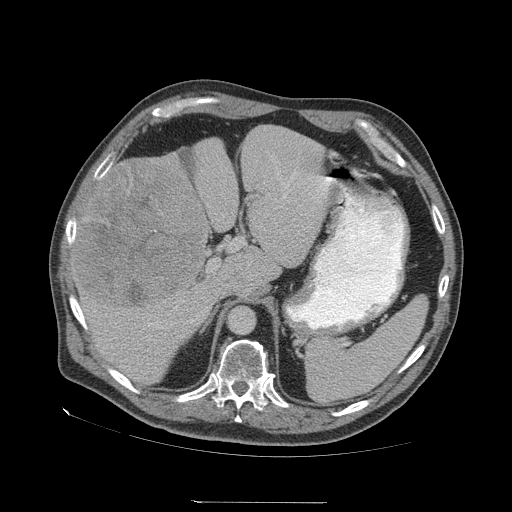
Contrast-enhanced abdominal CT (liver protocol), one axial slice. Slice 40 of 83 in the series (ordered by position). Reconstruction kernel STANDARD. 140 kVp. Soft-tissue window (W 400 / L 40 HU). 512 × 512 image matrix, field of view 460 × 460 mm. From the clinical record (not read from this slice): diagnosis: hepatocellular carcinoma (patient treated with transarterial chemoembolisation; whether this scan precedes or follows treatment is not stated here); TNM stage (as recorded): Stage-I; Child-Pugh class: A; tumour differentiation: well differentiated; tumour nodularity: uninodular.
Structures marked on this image (semi-automatically segmented with operator editing):
- liver parenchyma outside the tumour (the mass and vessels are separate outlines, so this box may not span the whole liver): box from (x=70, y=126) to (x=332, y=384) px
- mass: (x=76, y=160)–(x=208, y=310)
- liver vessels: (x=82, y=176)–(x=331, y=329)